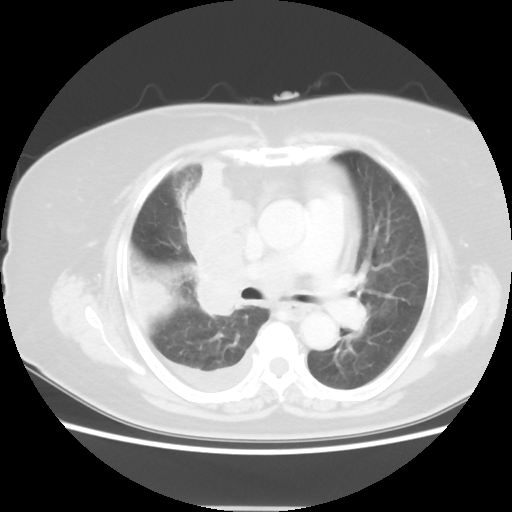
Chest CT, one axial slice; slice 30 of 48 in the series (ordered by position); reconstruction kernel STANDARD; 120 kVp; lung window (W 1500 / L -600 HU); 5 mm slice thickness; 512 × 512 image matrix, field of view 360 × 360 mm. Patient: female, 73 years. From the clinical record (not read from this slice): clinical TNM (as recorded): T3 N3 M1b; histopathological grade: G3.
Outlined on this slice (bounding box drawn by a radiologist):
- lung tumour (recorded histology: small cell carcinoma): bounding box (x1, y1, x2, y2) in pixels: (172, 149, 255, 322)